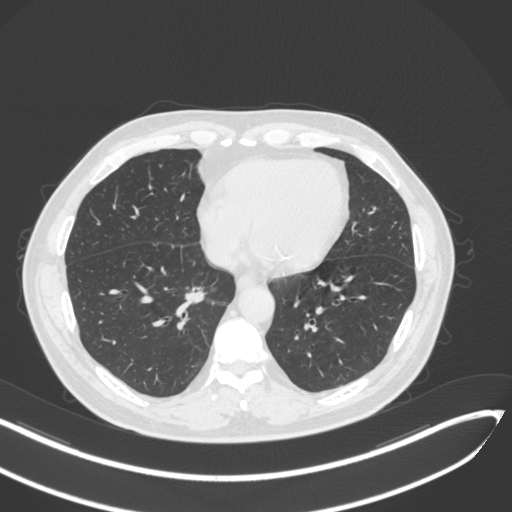
Chest CT, one axial slice; slice 134 of 429 in the series (ordered by position); reconstruction kernel B31f; lung window (W 1500 / L -600 HU); 1 mm slice thickness; 512 × 512 image matrix, field of view 400 × 400 mm. Patient: male, 62 years. Case-level facts recorded for this patient, not image findings: clinical TNM (as recorded): T1b N0 M0; histopathological grade: G2.
Annotated regions visible in this slice (rectangle marked by the reading radiologist):
- lung tumour (recorded histology: adenocarcinoma): bounding box [x1, y1, x2, y2] px = [182, 286, 212, 307]